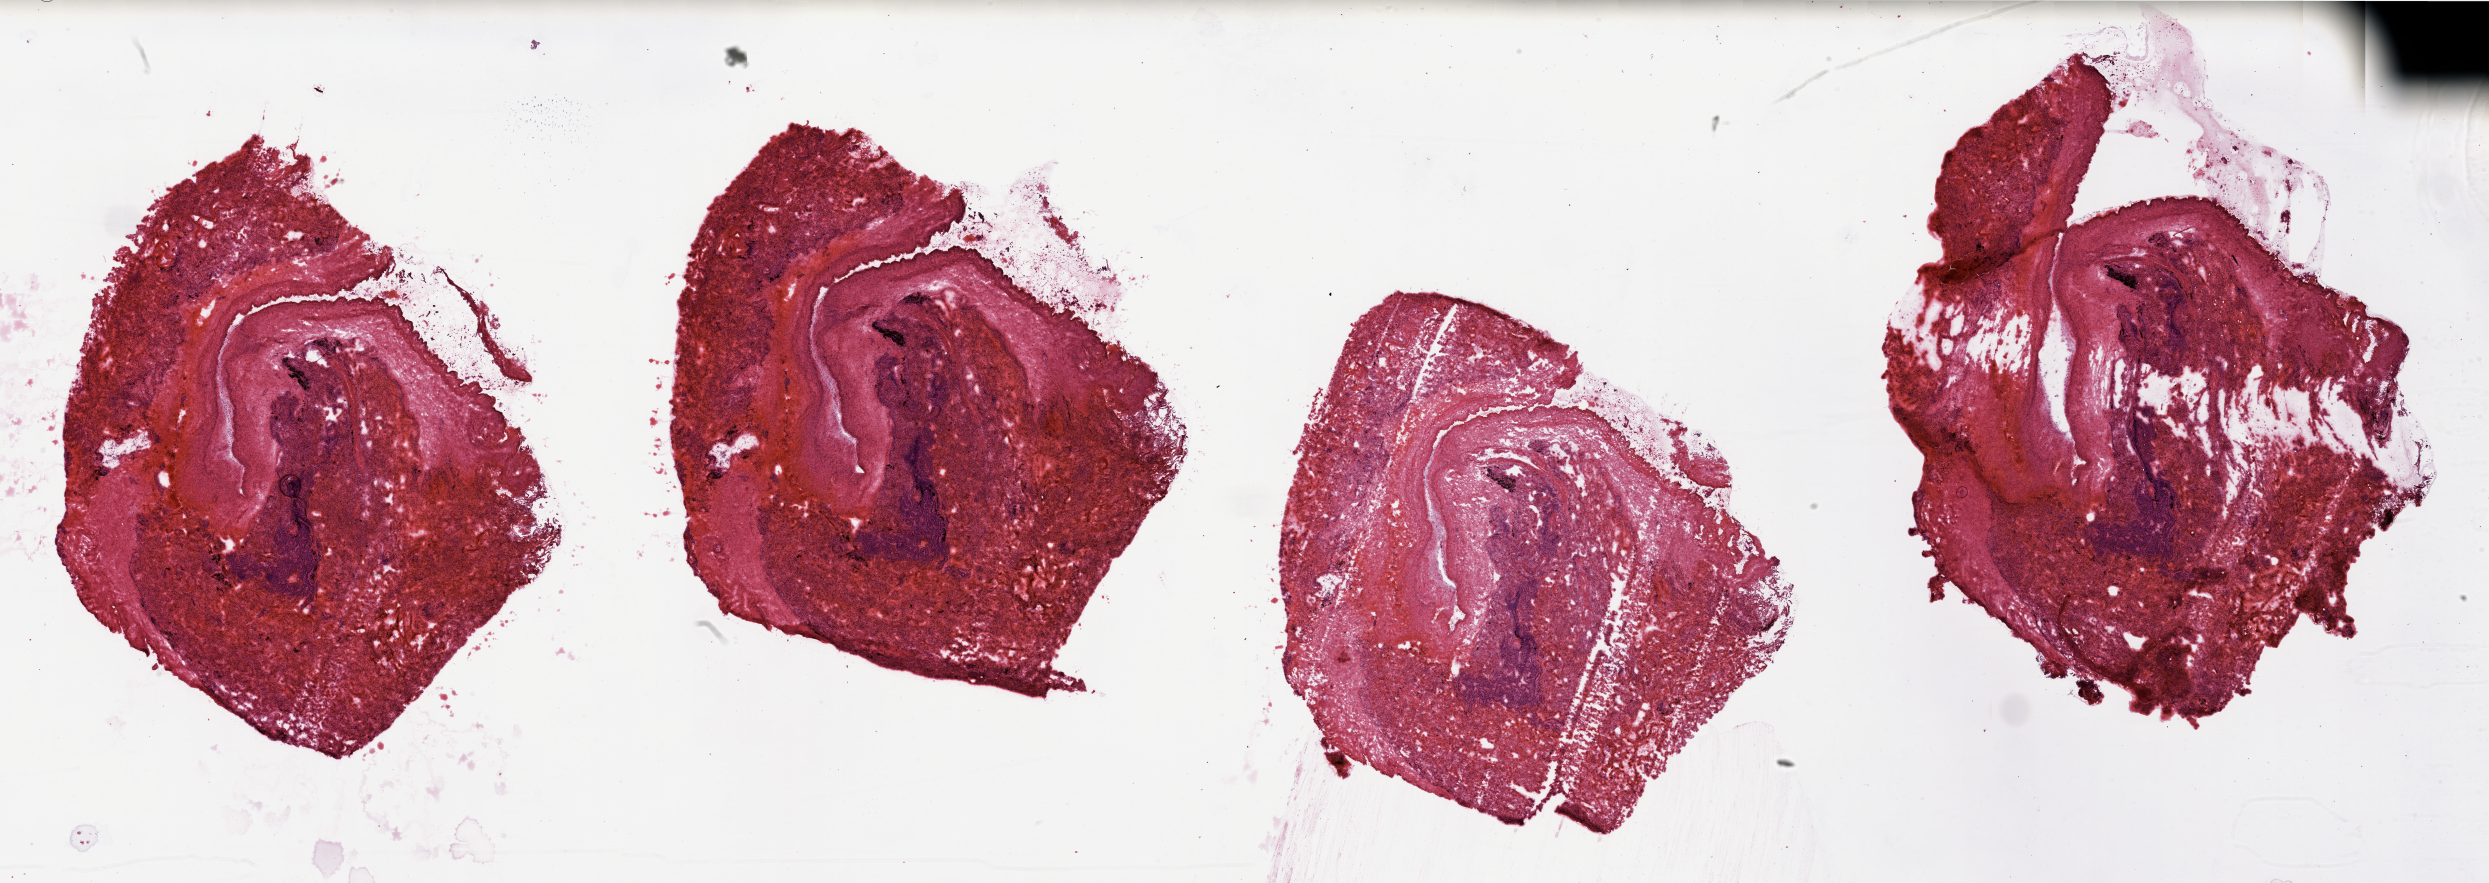
Digitized Hematoxylin and eosin (H&E) stained tissue section (whole slide), whole scanned area (about 39.4 x 14.0 mm) shown as a low-resolution overview. Tumour tissue sample, lung. 73-year-old male patient. Histologic grade: GX (grade cannot be assessed).
• diagnosis: Adenocarcinoma, NOS
• primary tumour site (as recorded): right upper lobe
• AJCC pathologic stage: IB